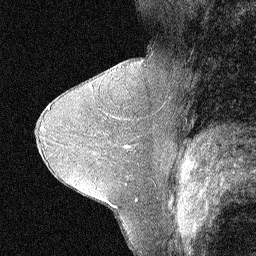
Breast MRI (dynamic contrast-enhanced), one sagittal slice; position 32 of 64 along the scan axis; dynamic contrast-enhanced study with each time point stored as its own series, time point 2 of 3 at this slice position (early post-contrast, ordered by acquisition time); 1.5 T; TE 4.5 ms, TR 11 ms; 256 × 256 image matrix, field of view 200 × 200 mm. Female patient, age 31 years. From the clinical record (not read from this slice): setting: breast cancer imaged before/during neoadjuvant chemotherapy; receptor status: HER2-positive.
Structures marked on this image (semi-automatic segmentation, software-assisted and operator-edited):
- analysis volume of interest (the breast-tissue region the enhancement analysis was run in; not a lesion): box from (x=88, y=117) to (x=152, y=183) px
- tumour enhancement mask (voxels above the 90 % enhancement threshold inside the analysis volume of interest): (x=127, y=146)–(x=131, y=147)